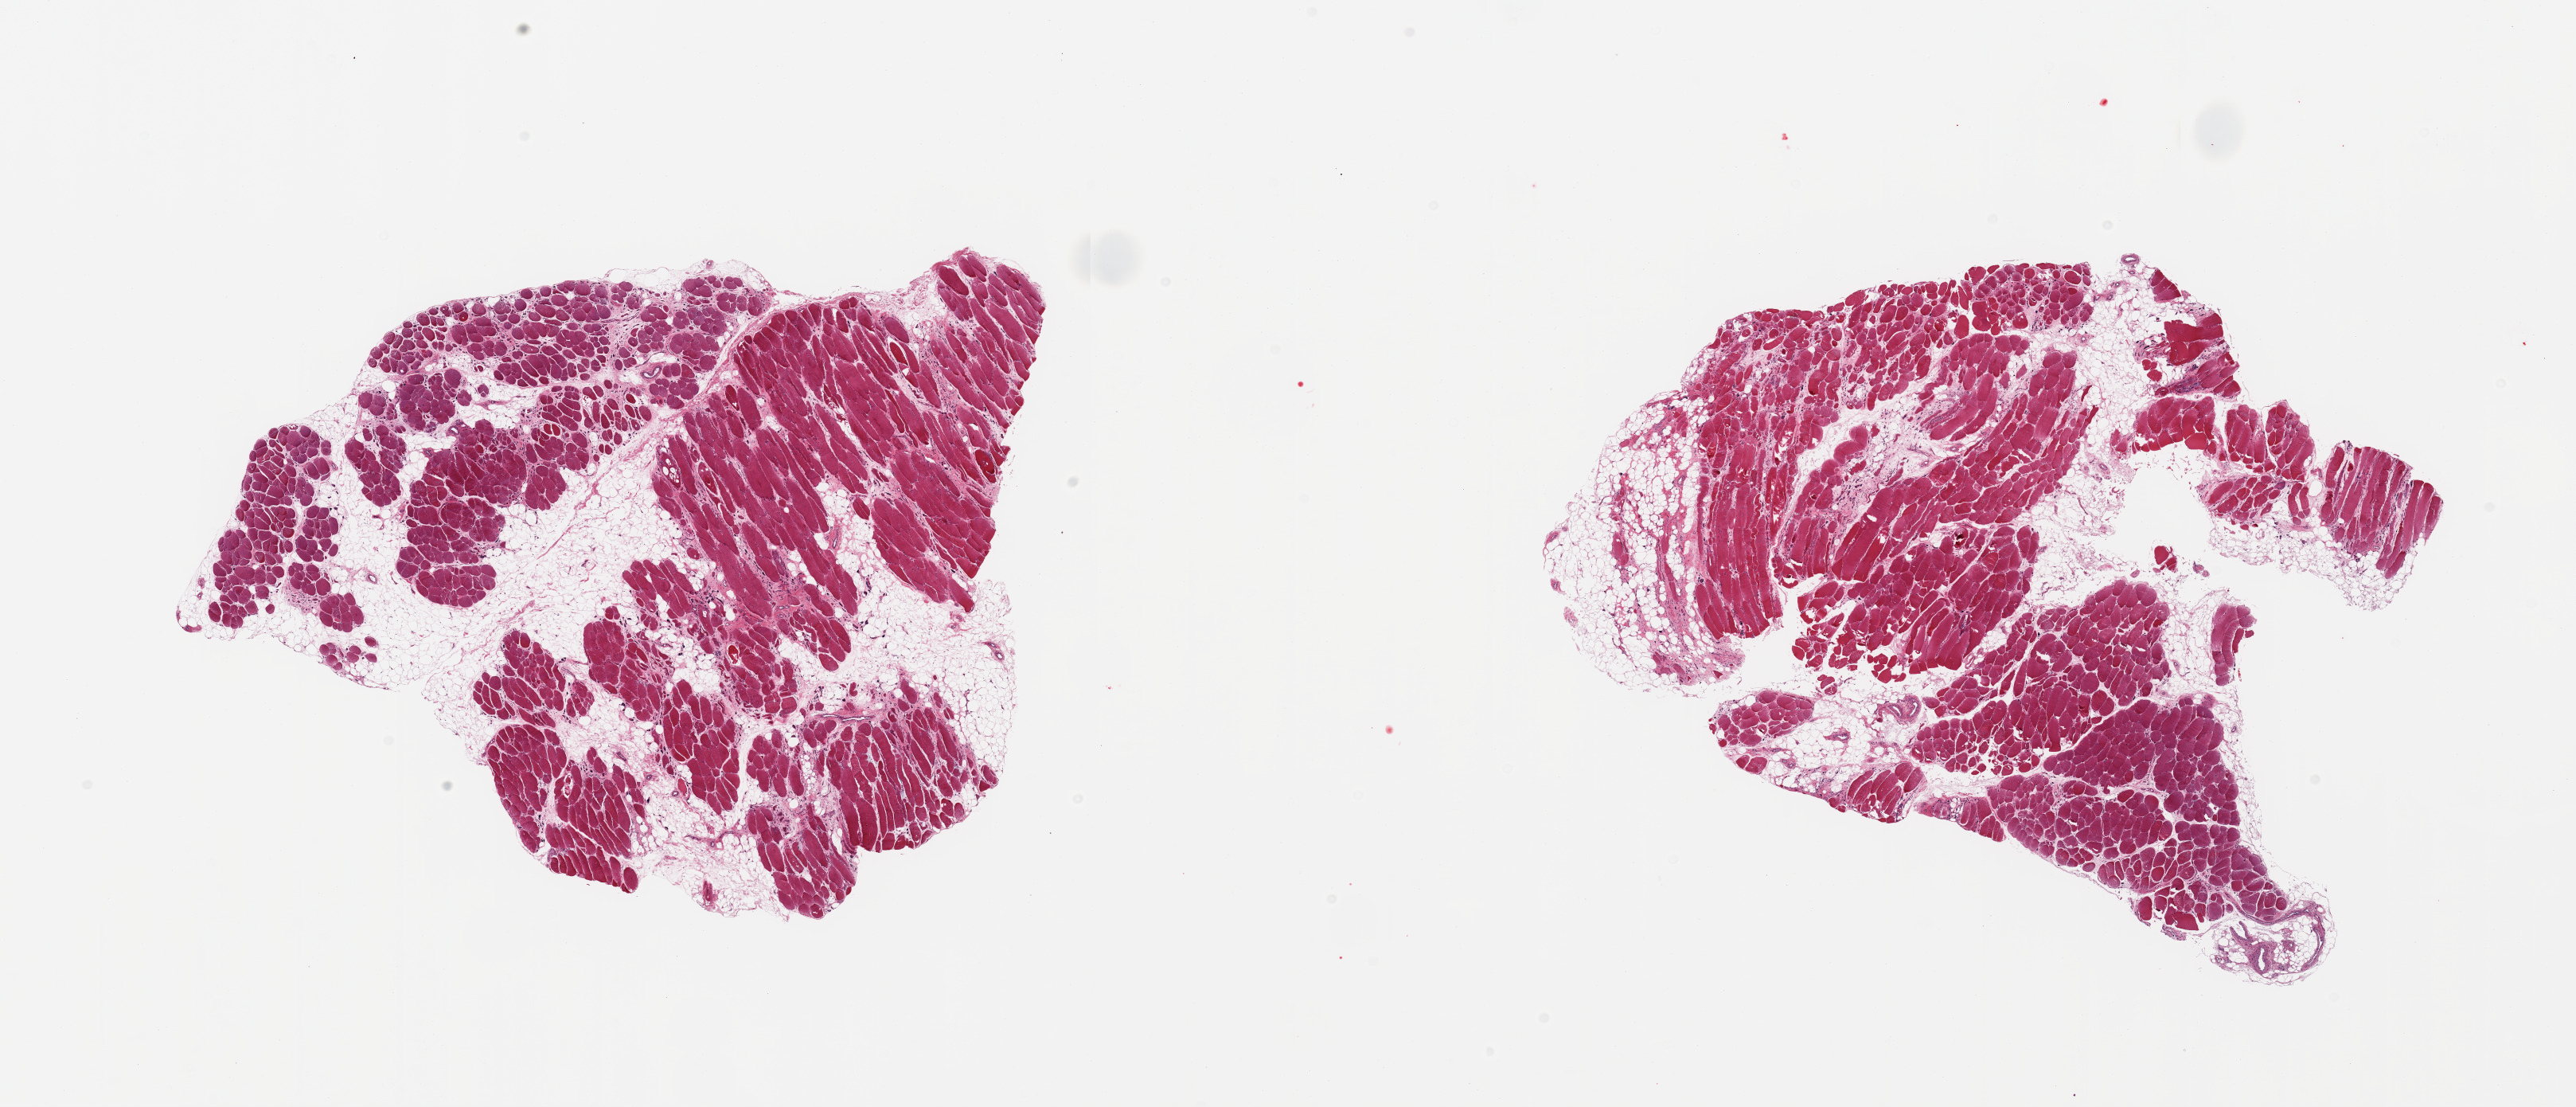
Whole-slide image, hematoxylin and eosin (H&E) stain — a low-resolution overview of the entire scanned area, about 25.6 x 11.0 mm, PAXgene-fixed paraffin-embedded (PFPE) section, section of skeletal muscle (target tissue), donor tissue sample. Male donor.
Review note (as recorded): 2 pieces, moderate fiber atrophy, ~30% interstitial fat.